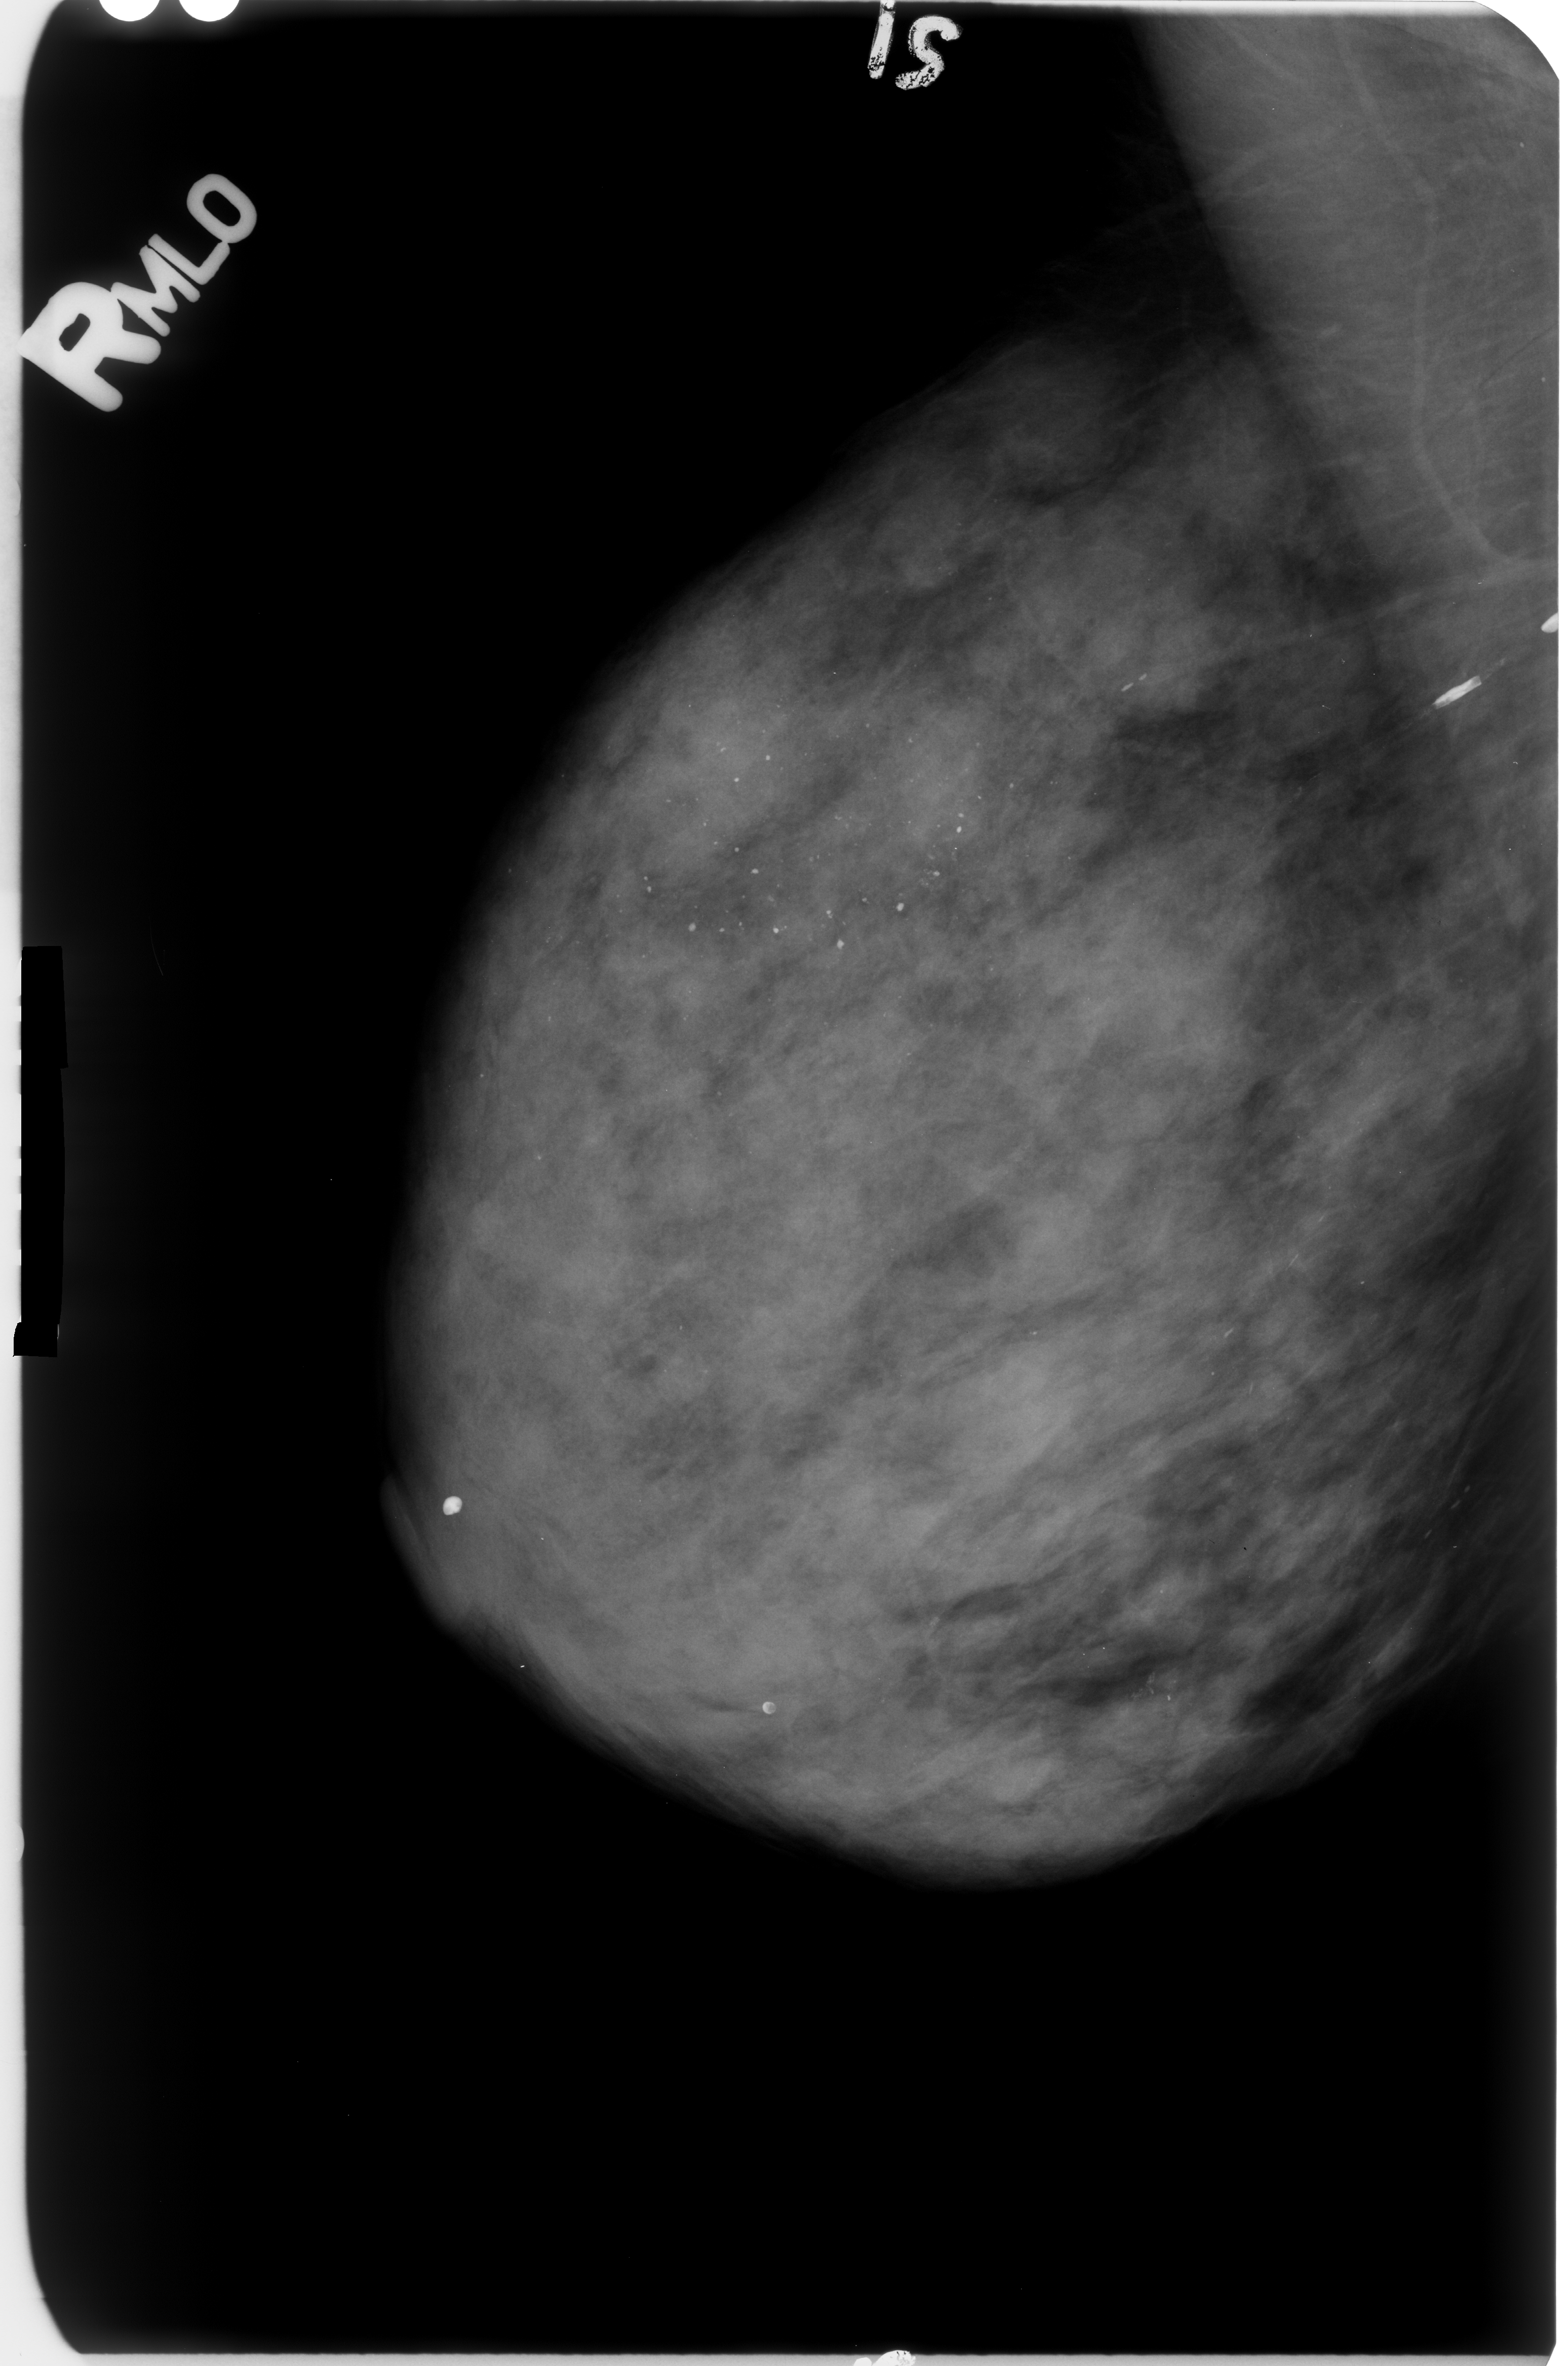
Mammogram (digitized film); right breast; MLO view; BI-RADS breast density category 4 (scale 1–4); 1568 × 2366 image matrix.
Expert-marked regions of interest on this film, with their recorded descriptors:
- Finding 1 of 2: calcifications, morphology vascular / coarse / lucent center / round and regular / punctate, distribution regional; BI-RADS assessment category 2; subtlety rating 5 on a 1 (subtle) to 5 (obvious) scale; outcome (as recorded, no biopsy): benign without callback (not worked up further): bounding box <623,656,1010,994> (left, top, right, bottom; pixels)
- Finding 2 of 2: calcifications, morphology vascular; BI-RADS assessment category 2; benign; no additional work-up was recommended (outcome (as recorded, no biopsy): benign without callback): <1422,595,1565,718>